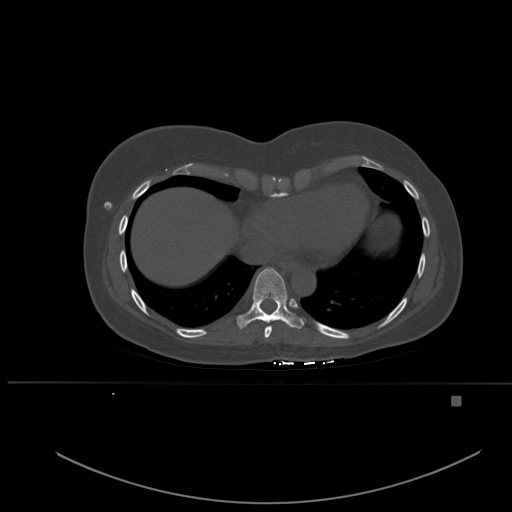
CT including the spine, one axial slice. Position 308 of 651 along the scan axis. Bone window (W 1800 / L 400 HU). 1.5 mm slice thickness. 512 × 512 image matrix, field of view 443 × 443 mm. Female patient, age 49 years. From the clinical record (not read from this slice): primary cancer: breast.
Outlined on this slice (semi-automatic segmentation, software-assisted and operator-edited):
- T8 vertebra: box from (x=264, y=326) to (x=272, y=338) px
- T9 vertebra: (x=236, y=268)–(x=304, y=333)